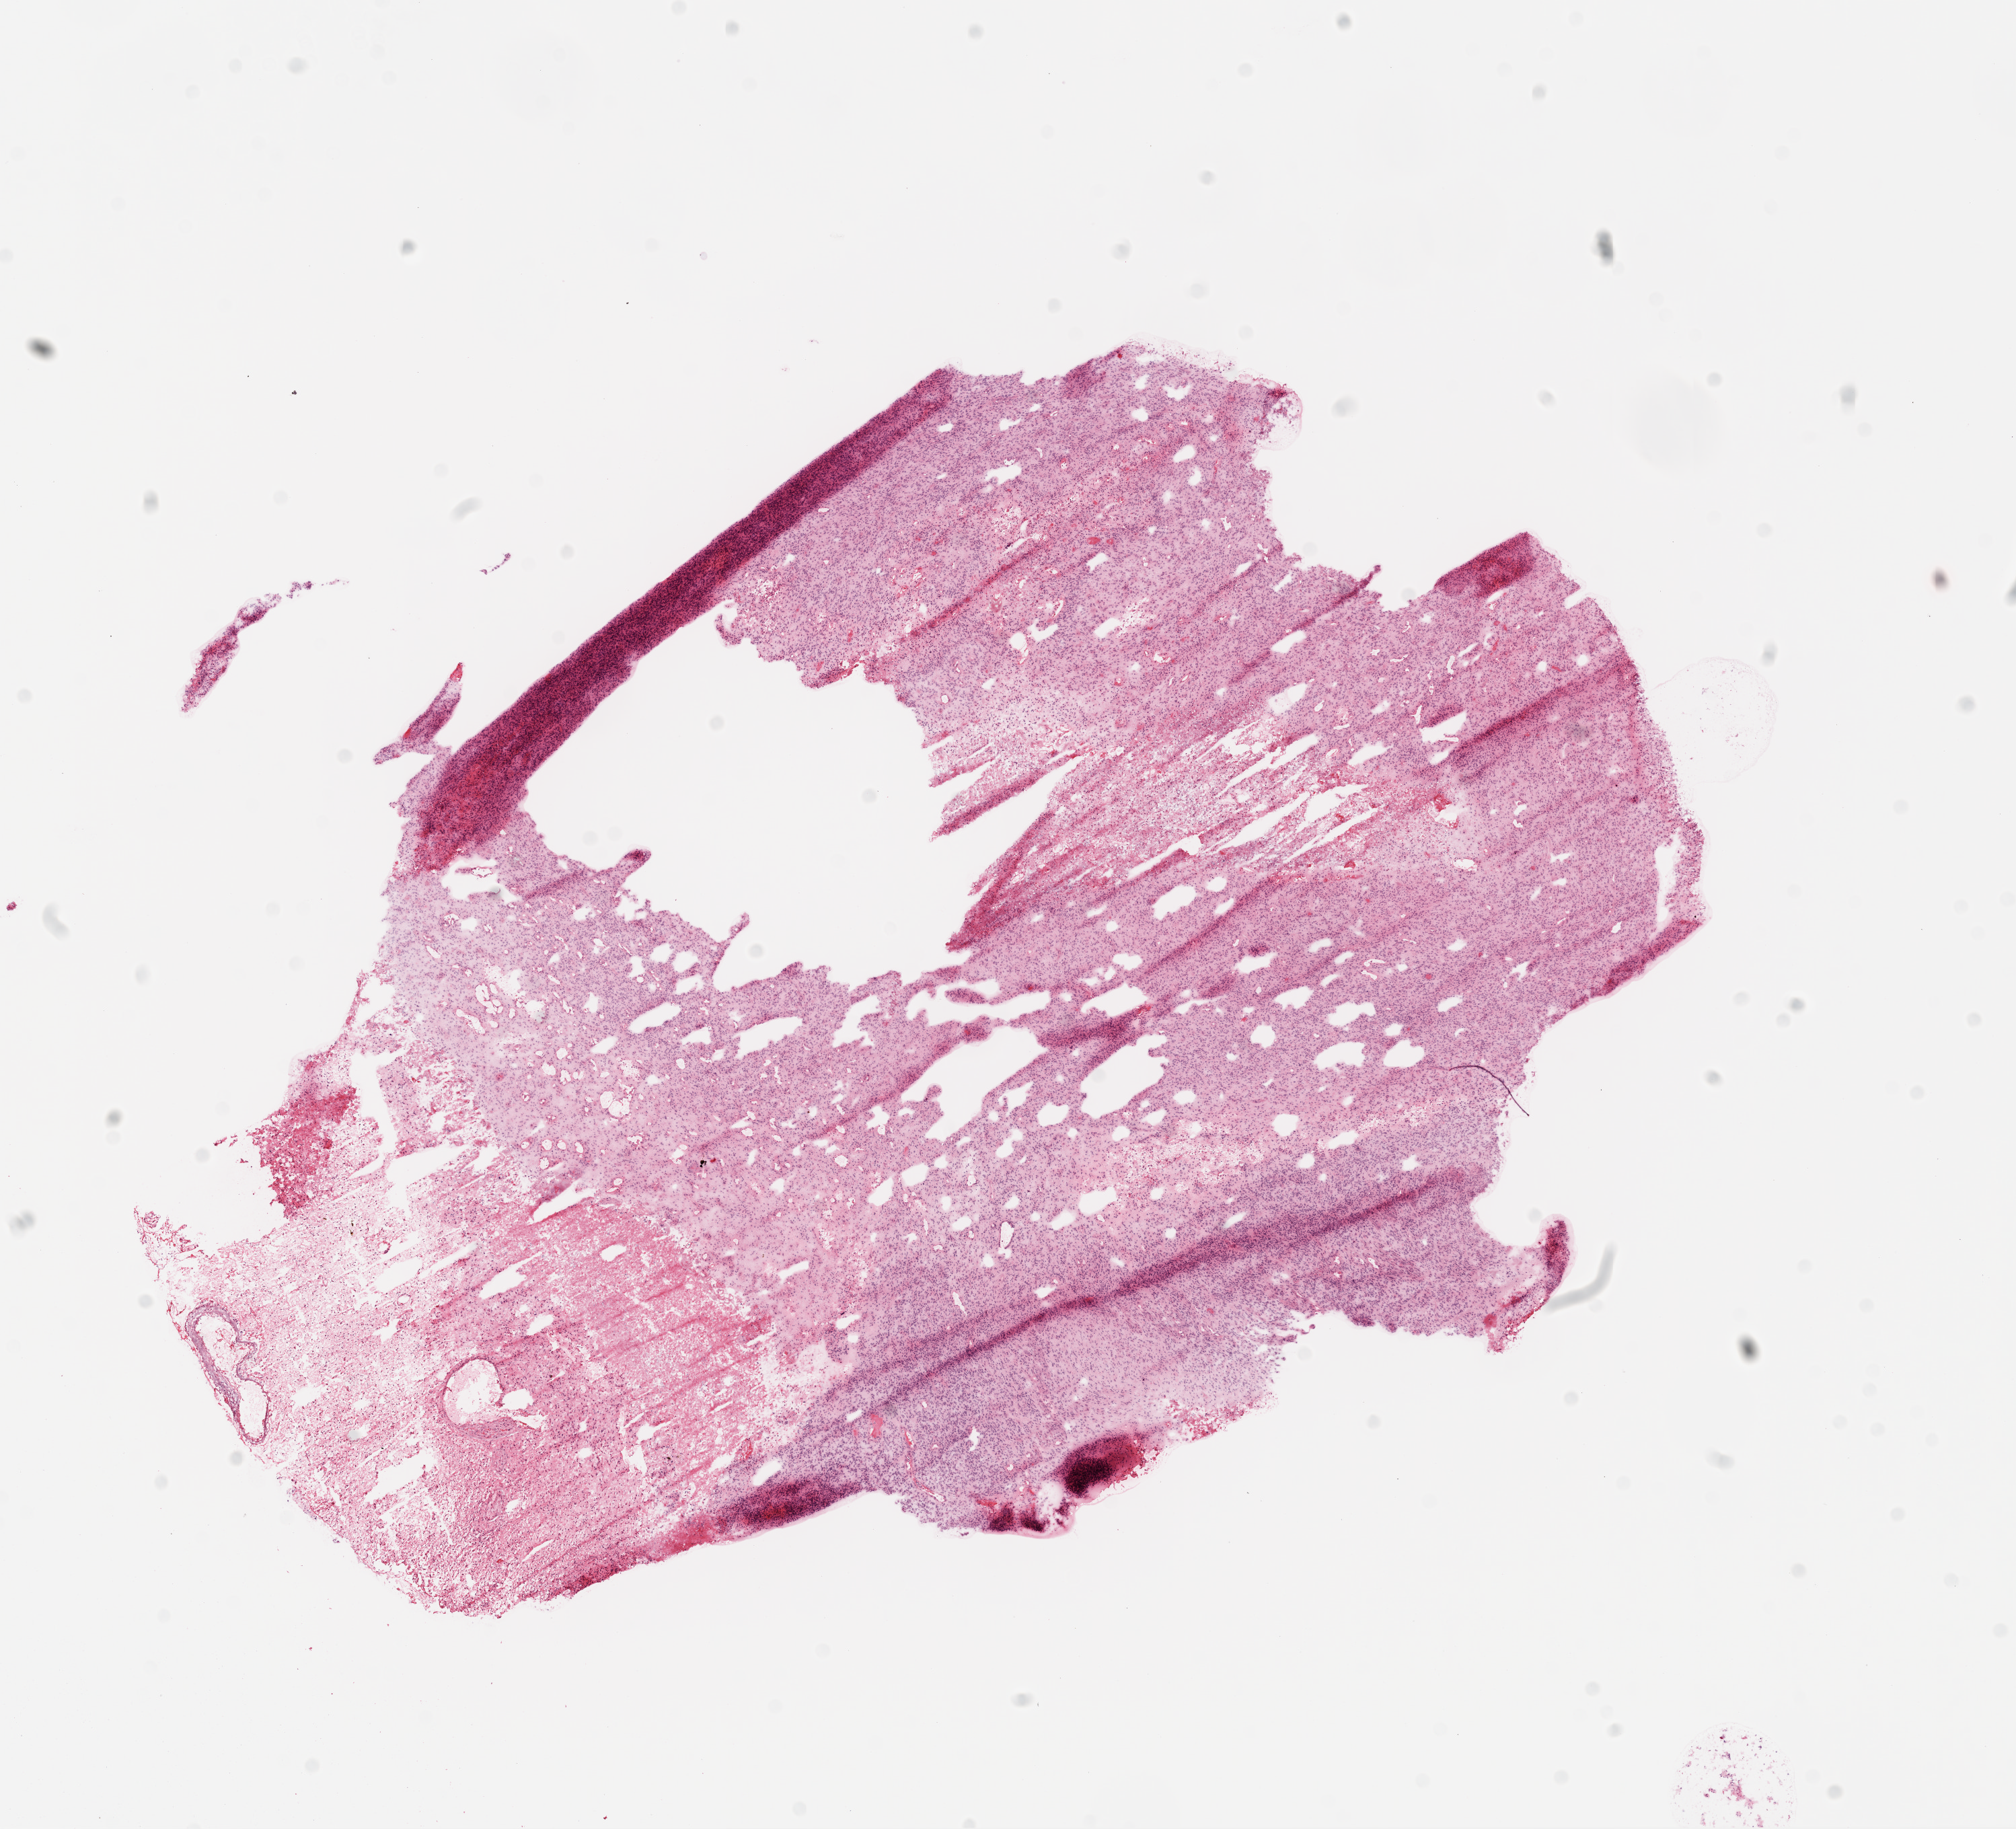
Digitized H&E tissue section (whole slide), shown as a low-resolution overview of the whole scanned area (about 12.1 x 11.0 mm). Frozen section from the top of the tissue portion. Primary tumour sample from the brain. Female, age 52 years at initial diagnosis. Composition of this section per pathologist review: tumour cells 75%, tumour nuclei 90%, normal cells 0%, stromal cells 5%, necrosis 20%.
Pathologic diagnosis: Glioblastoma.